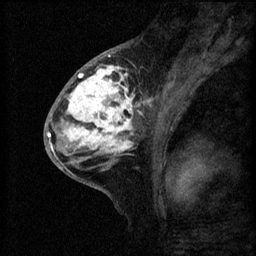
Breast MRI (dynamic contrast-enhanced), one sagittal slice. Position 30 of 60 along the scan axis. 3 images stored at this slice position (order not interpretable as contrast timing). 1.5 T. TE 4.2 ms, TR 8.2 ms. 256 × 256 image matrix, field of view 180 × 180 mm. Patient: female, 41 years.
Structures marked on this image (semi-automatically segmented with operator editing):
- analysis volume of interest (the breast-tissue region the enhancement analysis was run in; not a lesion): bounding box [x1, y1, x2, y2] px = [53, 62, 160, 175]
- tumour enhancement mask (voxels above the 70 % enhancement threshold inside the analysis volume of interest): [53, 66, 151, 165]